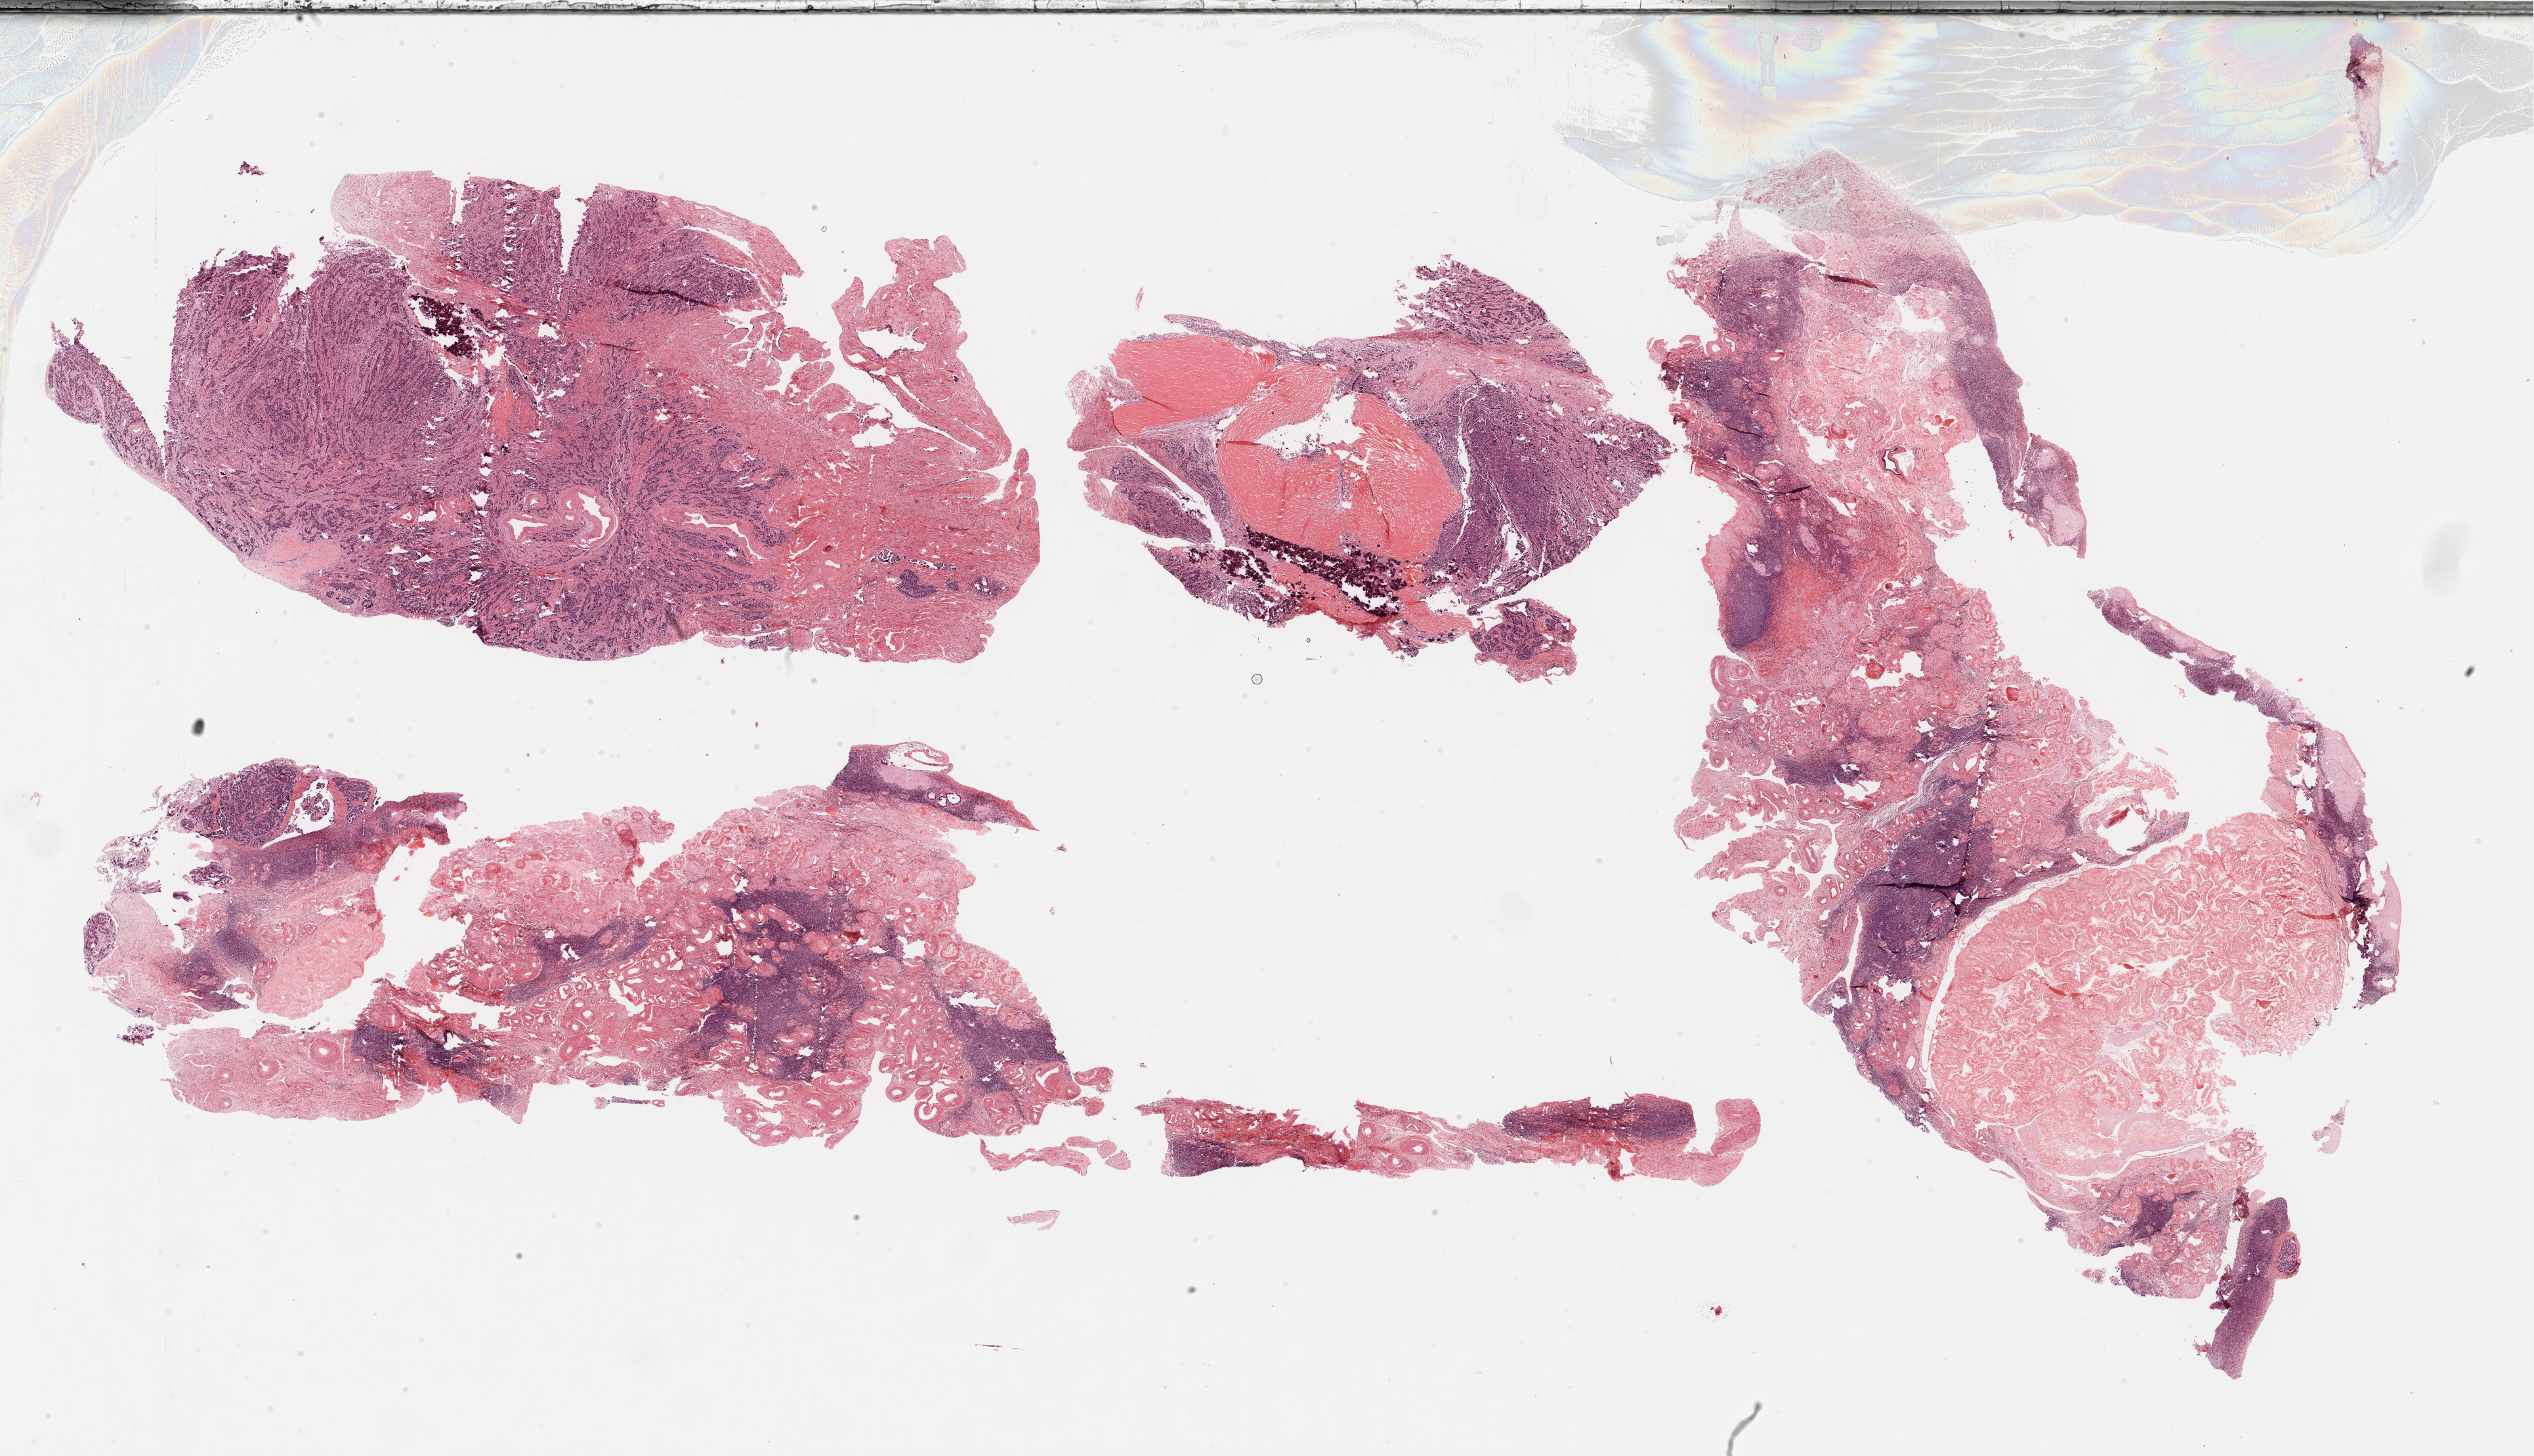
H&E-stained whole-slide image — shown as a low-resolution overview of the whole scanned area (about 31.2 x 17.9 mm, slide scanned at 40x), FFPE section, primary tumour sample from the ovary. Female patient; age at initial diagnosis 80 years.
Diagnosis: Serous cystadenocarcinoma, NOS.